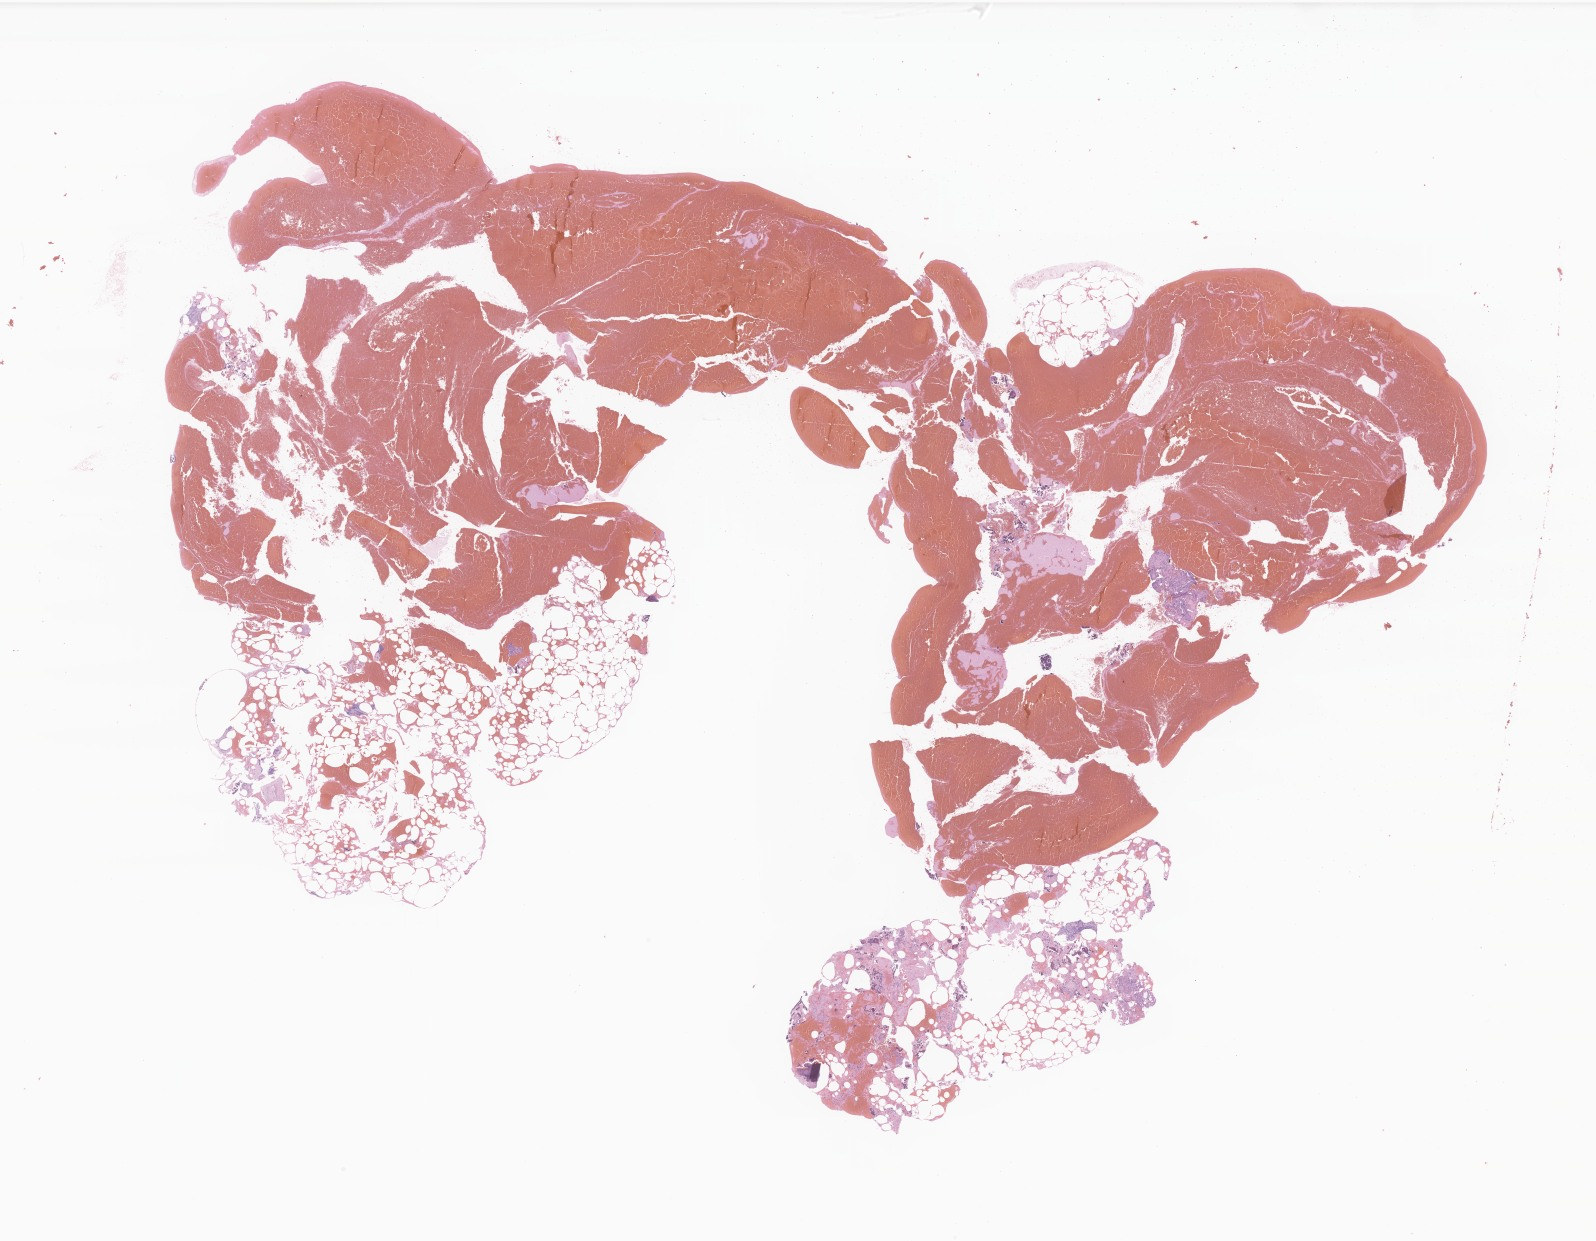
Haematoxylin and eosin whole-slide image of tumor tissue from the brain, low-resolution overview of the scanned area, about 26.9 x 20.9 mm; formalin-fixed, paraffin-embedded (FFPE) tissue. Female patient, age 144 months (12 years).
Diagnosis: Dysgerminoma.